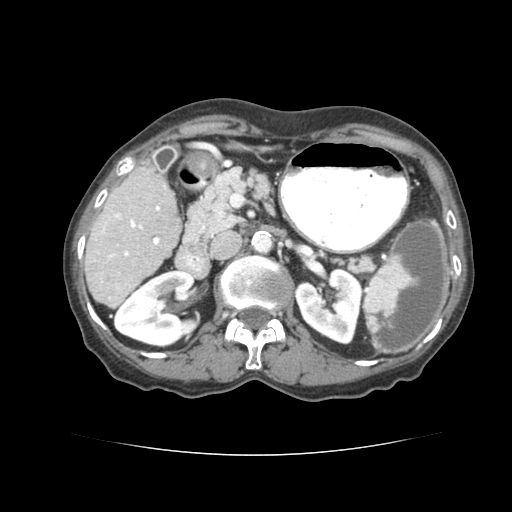
Contrast-enhanced abdominal CT (liver protocol), one axial slice; position 31 of 77 along the scan axis; 120 kVp; soft-tissue window (W 400 / L 40 HU); 2.5 mm slice thickness; 512 × 512 image matrix, field of view 340 × 340 mm. Case-level facts recorded for this patient, not image findings: diagnosis: hepatocellular carcinoma (patient treated with transarterial chemoembolisation; whether this scan precedes or follows treatment is not stated here); TNM stage (as recorded): Stage-I; Child-Pugh class: A; tumour differentiation: well differentiated; tumour nodularity: uninodular.
Annotated regions visible in this slice (semi-automatically segmented with operator editing):
- liver parenchyma outside the tumour (the mass and vessels are separate outlines, so this box may not span the whole liver): bounding box <84,157,180,302> (left, top, right, bottom; pixels)
- liver vessels: <152,202,159,241>